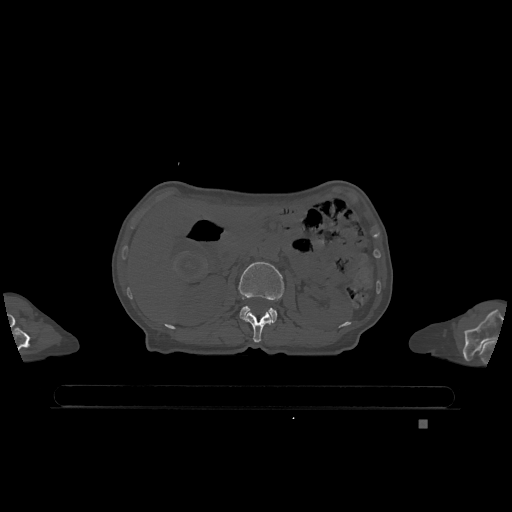
CT including the spine, one axial slice. Position 443 of 1317 along the scan axis. Bone window (W 1800 / L 400 HU). 512 × 512 image matrix. Patient: female, 74 years. From the clinical record (not read from this slice): primary cancer: lung; vertebrae with lytic lesions (as recorded): T1, T4, T5, T6, L4, L5.
Structures marked on this image (semi-automatically segmented with operator editing):
- L1 vertebra: bounding box <244,311,272,343> (left, top, right, bottom; pixels)
- L2 vertebra: <238,262,285,323>